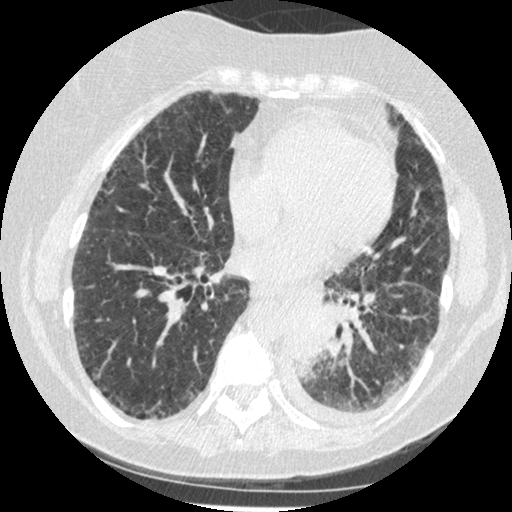
Low-dose screening chest CT, one axial slice; slice 90 of 341 in the series (ordered by position); 120 kVp; lung window (W 1500 / L -600 HU); 512 × 512 image matrix, field of view 310 × 310 mm.
Outlined on this slice (expert manual segmentation):
- lesion 1 (tumor, lower lobe of left lung): bounding box [x1, y1, x2, y2] px = [290, 314, 327, 371]